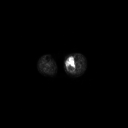
FDG PET of an extremity soft-tissue mass (from a PET/CT study), one axial slice. Slice 137 of 223 in the series (ordered by position). 3.27 mm slice thickness. 128 × 128 image matrix, field of view 700 × 700 mm. Patient: female, 70 years. From the clinical record (not read from this slice): histological type: extraskeletal high grade osteogenic sarcoma; grade: high; site of the primary tumour: left calf.
Annotated regions visible in this slice (expert contour drawn on MRI and transferred to this co-registered scan by the dataset authors):
- gross tumour volume (mass): bounding box <66,59,75,70> (left, top, right, bottom; pixels)